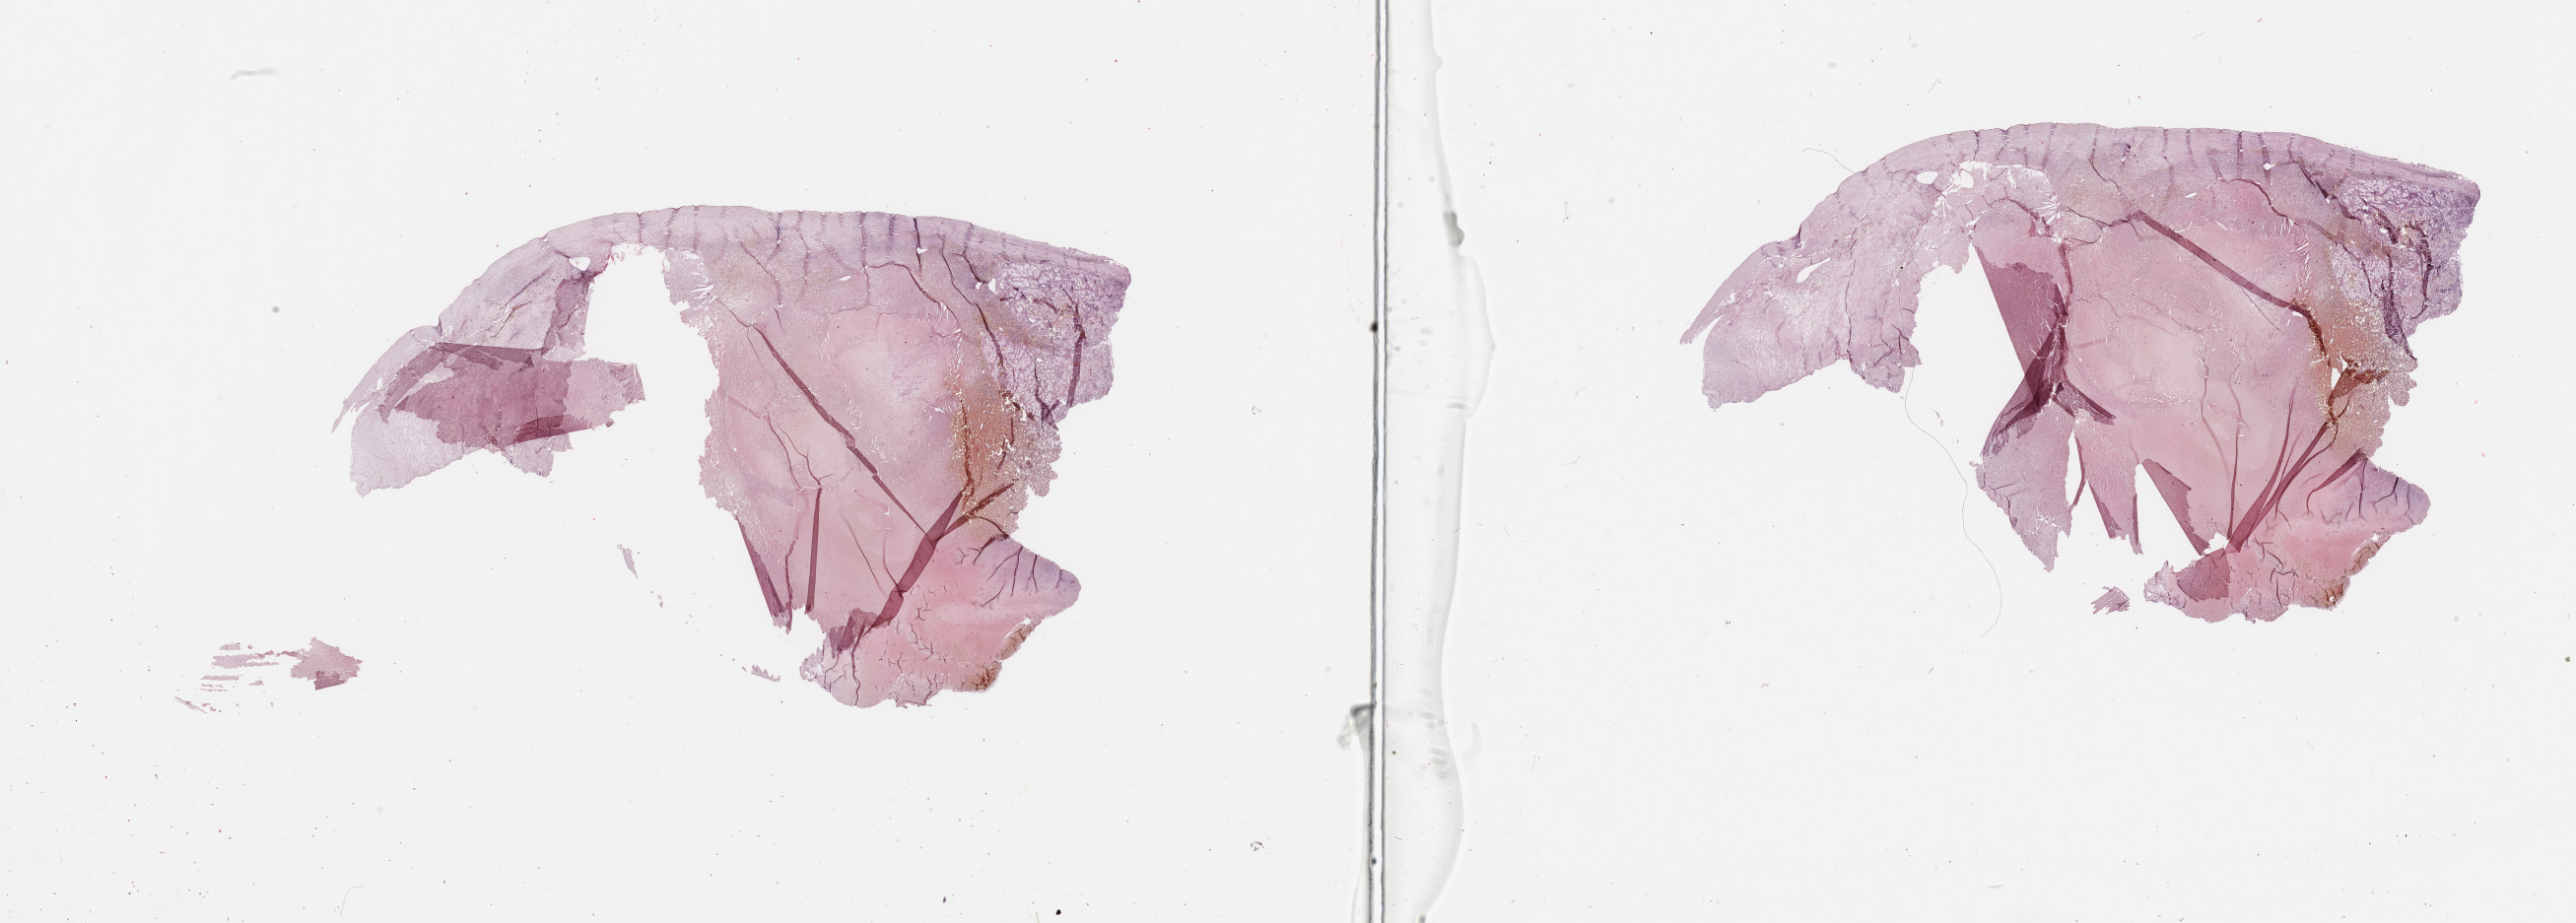
Whole-slide histology image, H&E-stained, whole scanned area (about 41.3 x 14.8 mm, slide scanned at 20x) shown as a low-resolution overview; kidney, tumour tissue. 86-year-old female patient. Histologic grade: G3 (poorly differentiated).
• diagnosis: Renal cell carcinoma, NOS
• primary tumour site (as recorded): upper pole
• AJCC pathologic stage: IV